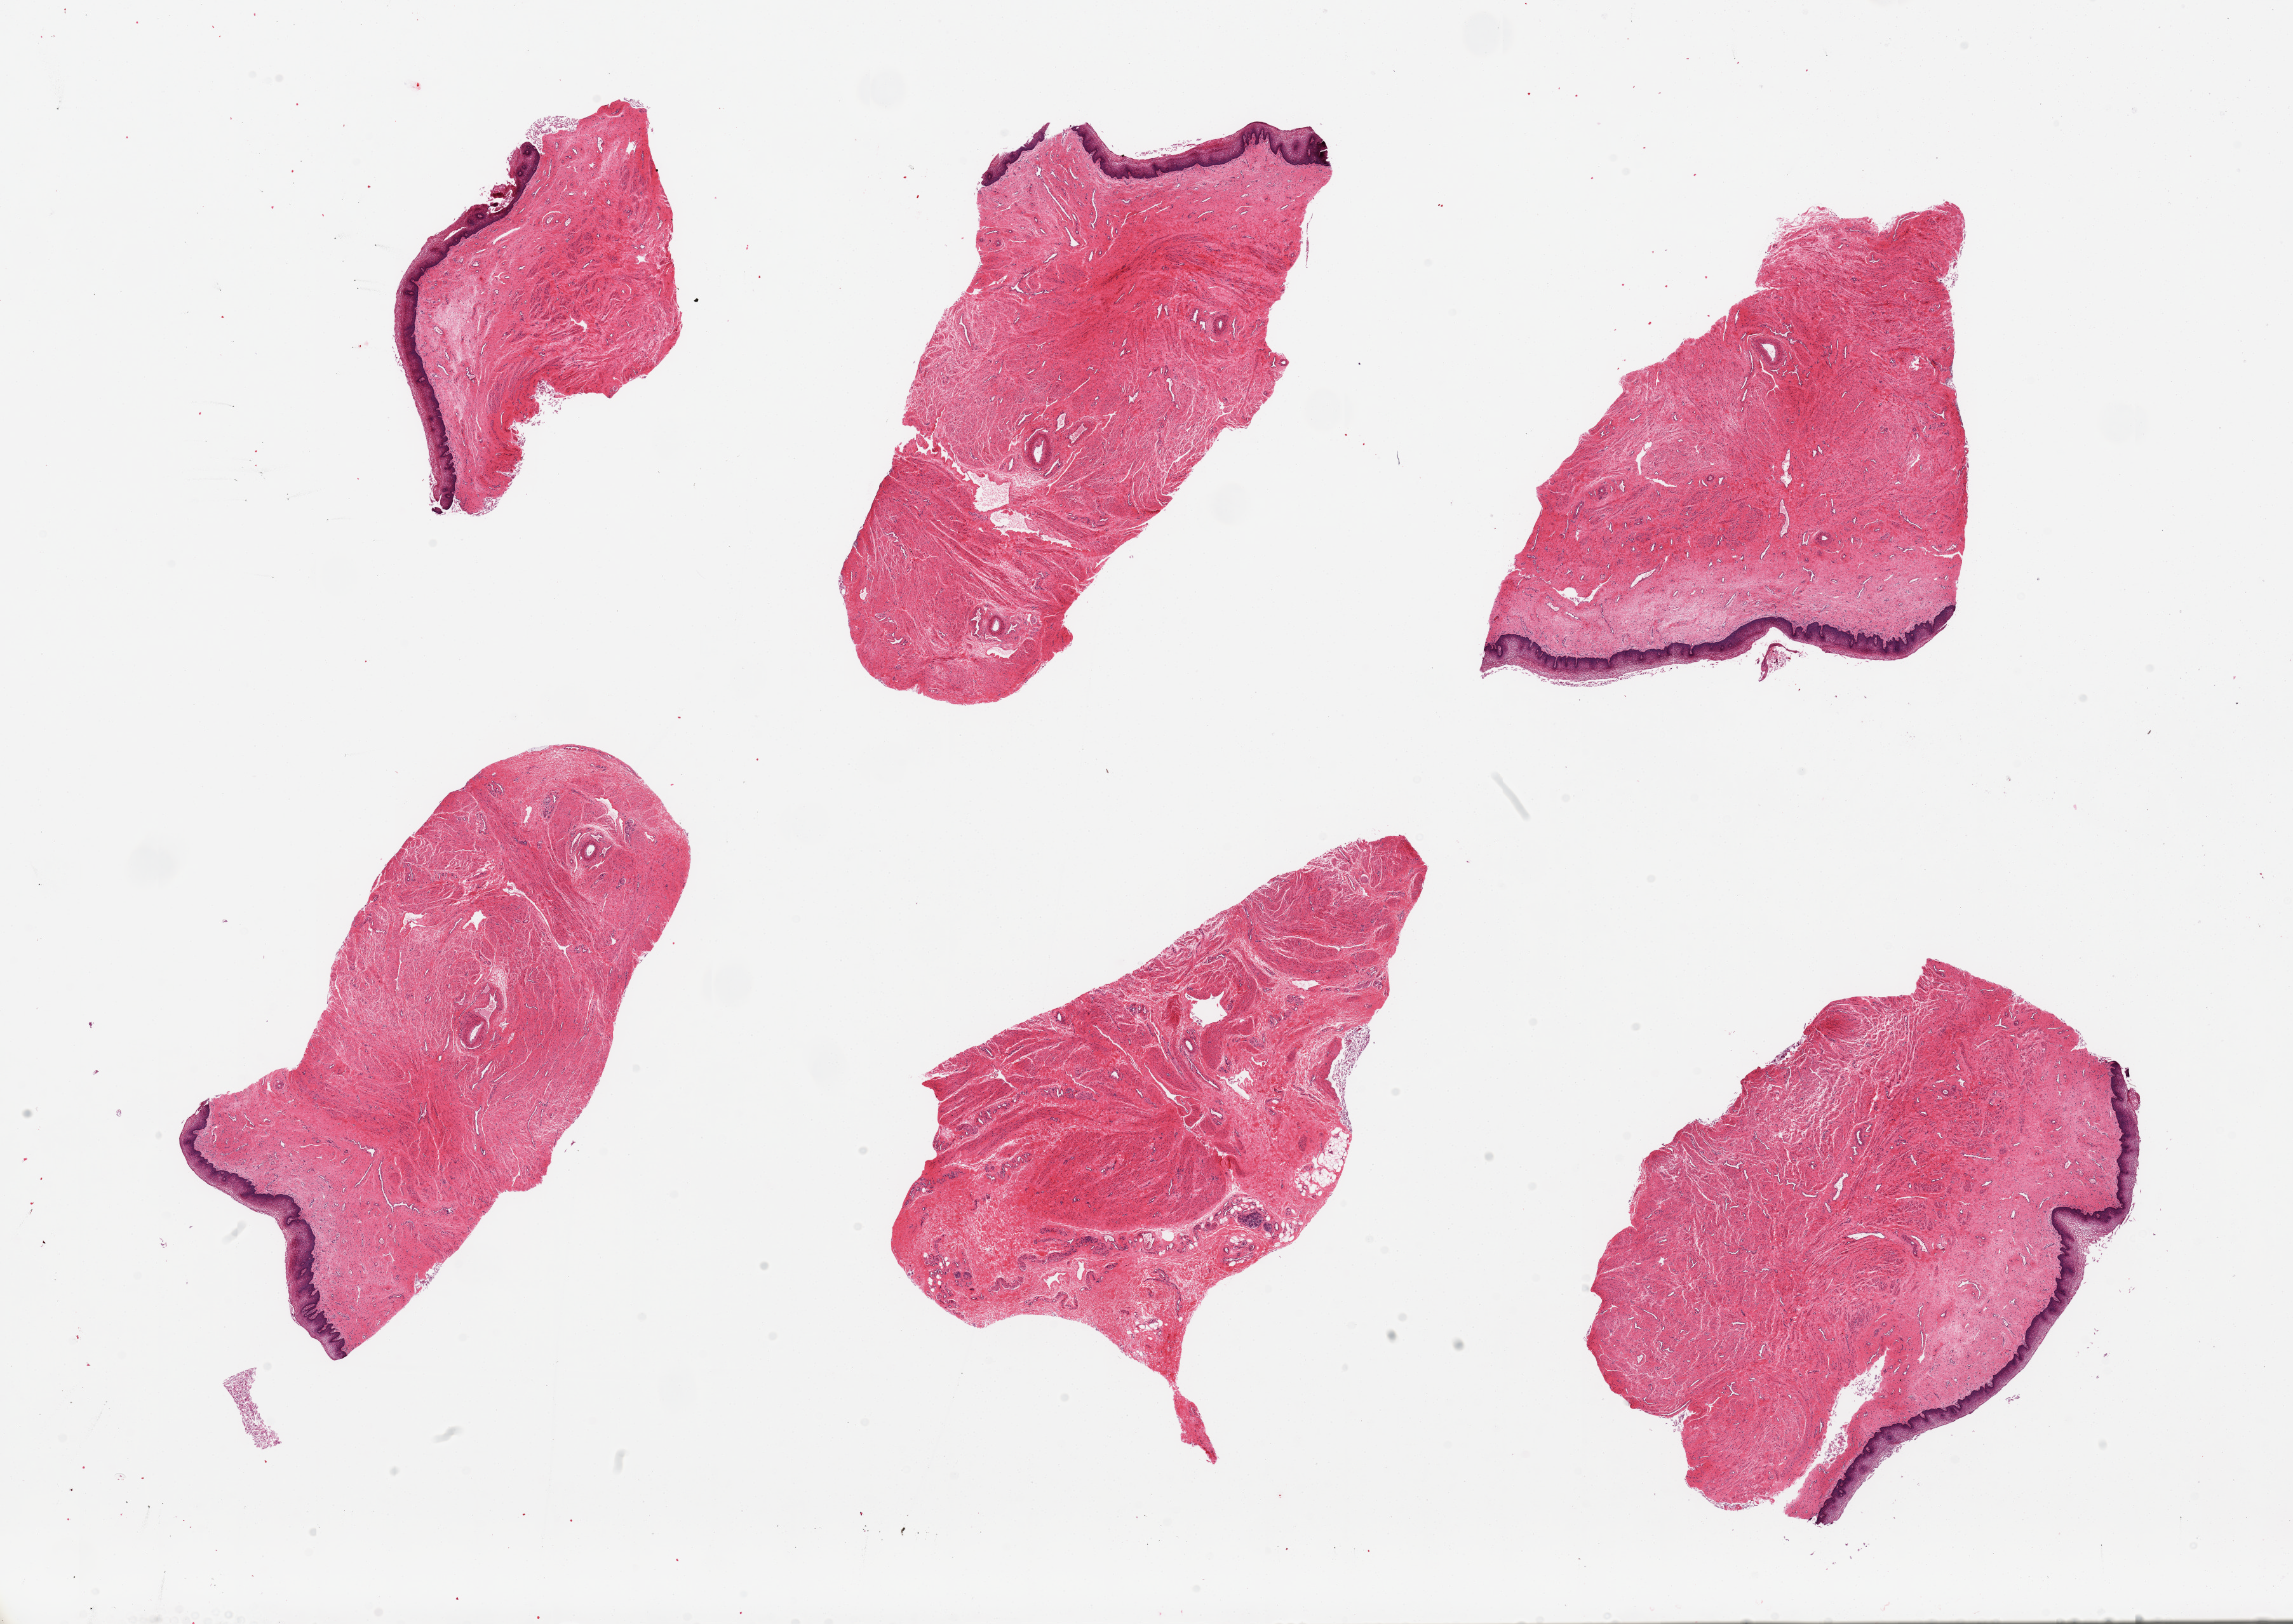
Digitized hematoxylin and eosin (H&E)-stained section — a low-resolution overview of the entire scanned area, about 28.5 x 20.2 mm (acquisition: 20x scan), PAXgene-fixed, paraffin-embedded tissue, target tissue: vagina, donor tissue sample. Female donor.
Reviewer comment on this tissue sample: 6 pieces.